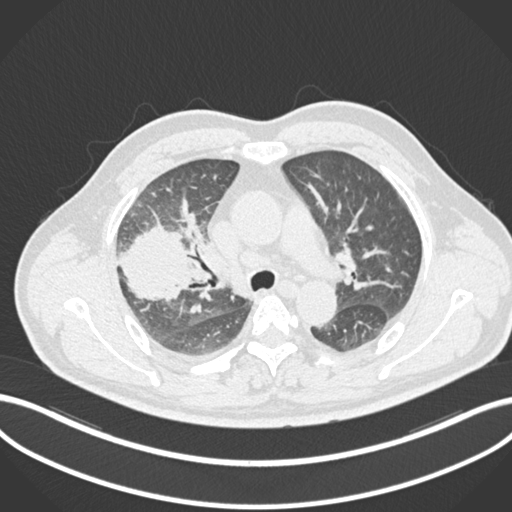
Chest CT, one axial slice. Position 654 of 852 along the scan axis. 120 kVp. Lung window (W 1500 / L -600 HU). 512 × 512 image matrix, field of view 400 × 400 mm. Male patient, age 55 years. Case-level facts recorded for this patient, not image findings: clinical TNM (as recorded): T3 N2 M1.
Annotated regions visible in this slice (rectangle marked by the reading radiologist):
- lung tumour (recorded histology: adenocarcinoma): bounding box [x1, y1, x2, y2] px = [115, 225, 195, 305]